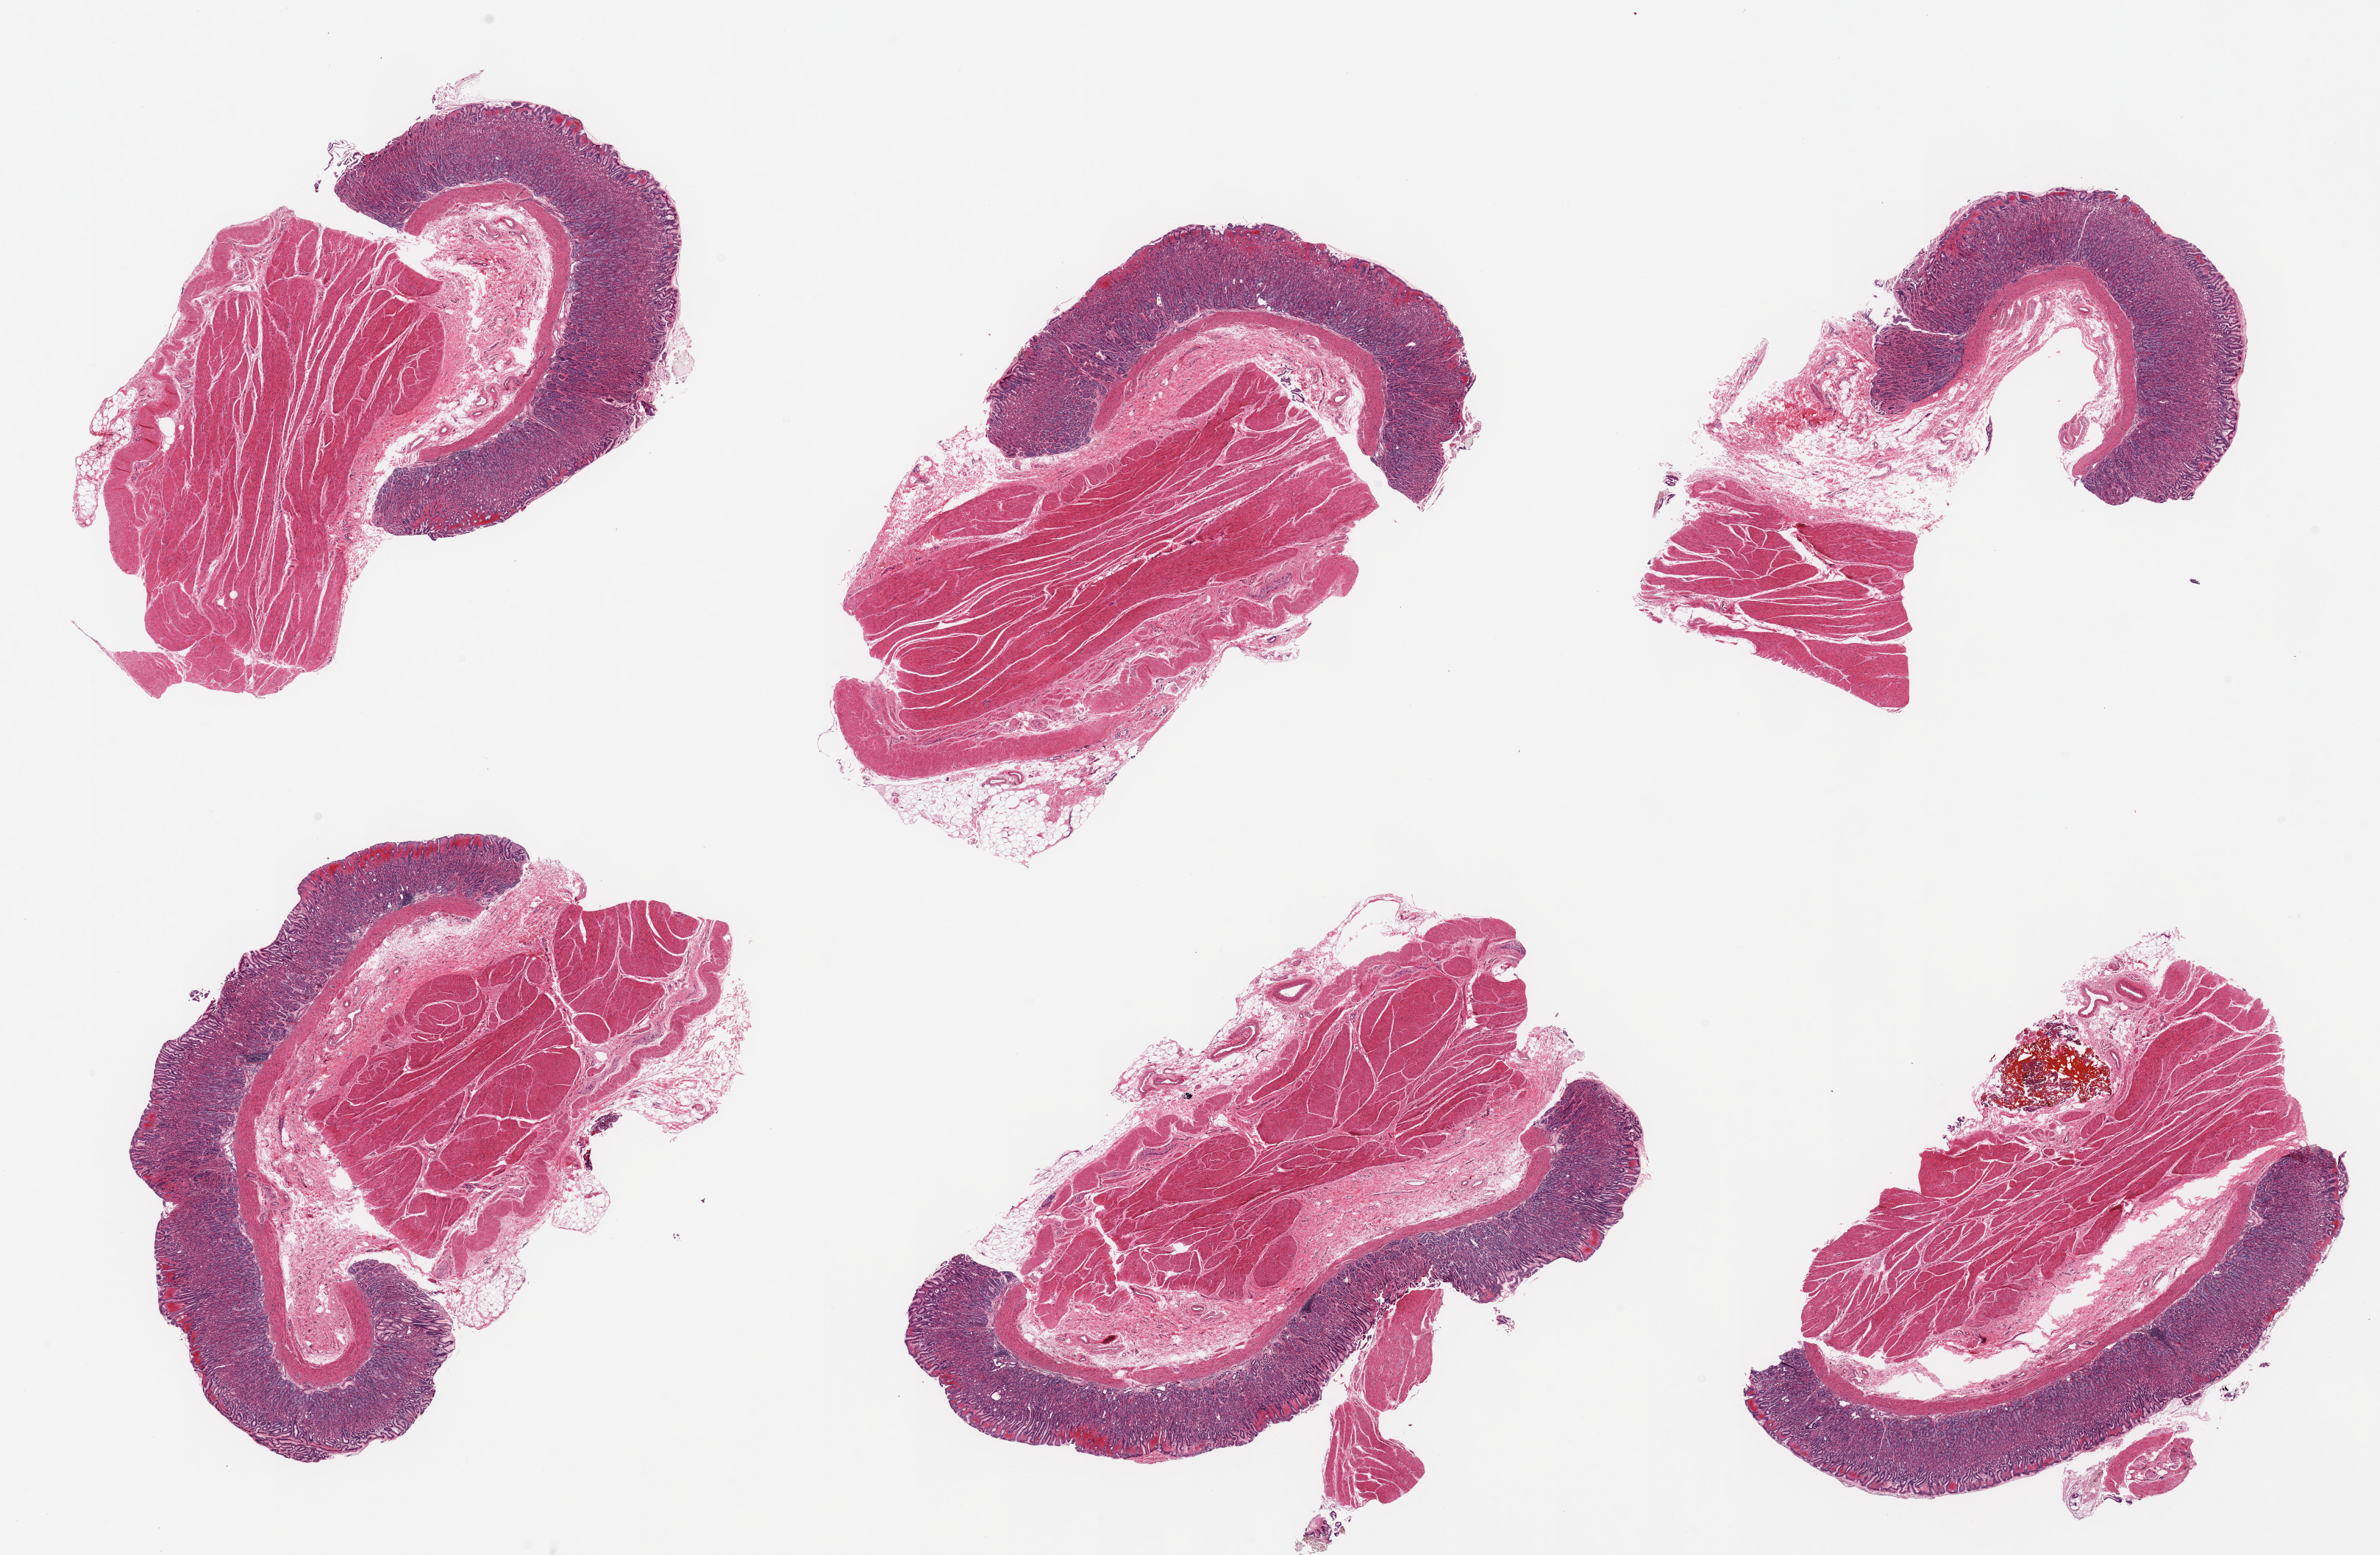
Whole-slide image, hematoxylin and eosin (H&E) stain, shown as a low-resolution overview of the whole scanned area (about 25.6 x 16.7 mm); PAXgene-fixed, paraffin-embedded tissue; target tissue: stomach; donor tissue sample.
* review note (as recorded): 6 pieces; full thickness sections, some superficial hemorrhage